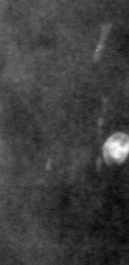
Cropped region of a digitized screen-film mammogram centred on a radiologist-marked abnormality; right breast; CC view.
Finding: calcifications, morphology pleomorphic, distribution clustered; BI-RADS assessment category 4; subtlety rating 2 on a 1 (subtle) to 5 (obvious) scale; pathology result (as recorded, not read from the image): malignant.